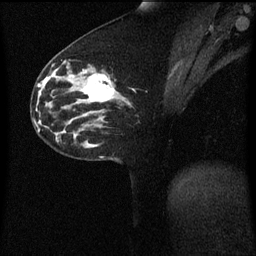
Breast MRI (dynamic contrast-enhanced), one sagittal slice. Dynamic contrast-enhanced series, image 2 of 3 at this slice position (ordered by acquisition). 1.5 T. TE 4.2 ms, TR 8.4 ms. 2 mm slice thickness. 256 × 256 image matrix, field of view 200 × 200 mm. Patient: female, 33 years. Case-level facts recorded for this patient, not image findings: setting: breast cancer imaged before/during neoadjuvant chemotherapy; receptor status: triple-negative.
Annotated regions visible in this slice (semi-automatically segmented with operator editing):
- analysis volume of interest (the breast-tissue region the enhancement analysis was run in; not a lesion): bounding box (x1, y1, x2, y2) in pixels: (76, 64, 123, 113)
- tumour enhancement mask (voxels above the 70 % enhancement threshold inside the analysis volume of interest): (81, 74, 114, 103)